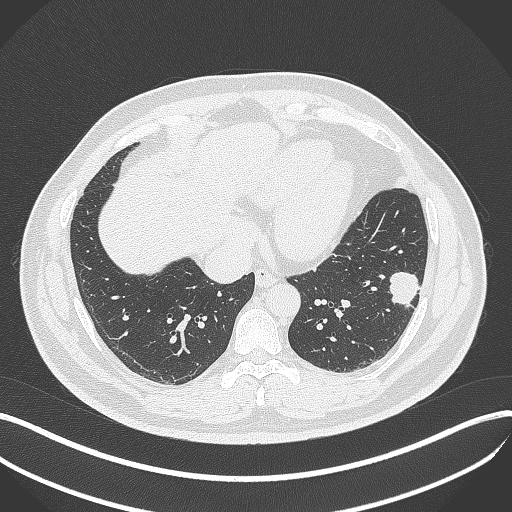
Chest CT, one axial slice; slice 137 of 429 in the series (ordered by position); reconstruction kernel B70f; 120 kVp; lung window (W 1500 / L -600 HU); 1 mm slice thickness; 512 × 512 image matrix, field of view 400 × 400 mm. Patient: male, 39 years. From the clinical record (not read from this slice): clinical TNM (as recorded): T2a N0 M0.
Annotated regions visible in this slice (bounding box drawn by a radiologist):
- lung tumour (recorded histology: adenocarcinoma): bounding box (x1, y1, x2, y2) in pixels: (384, 264, 422, 311)